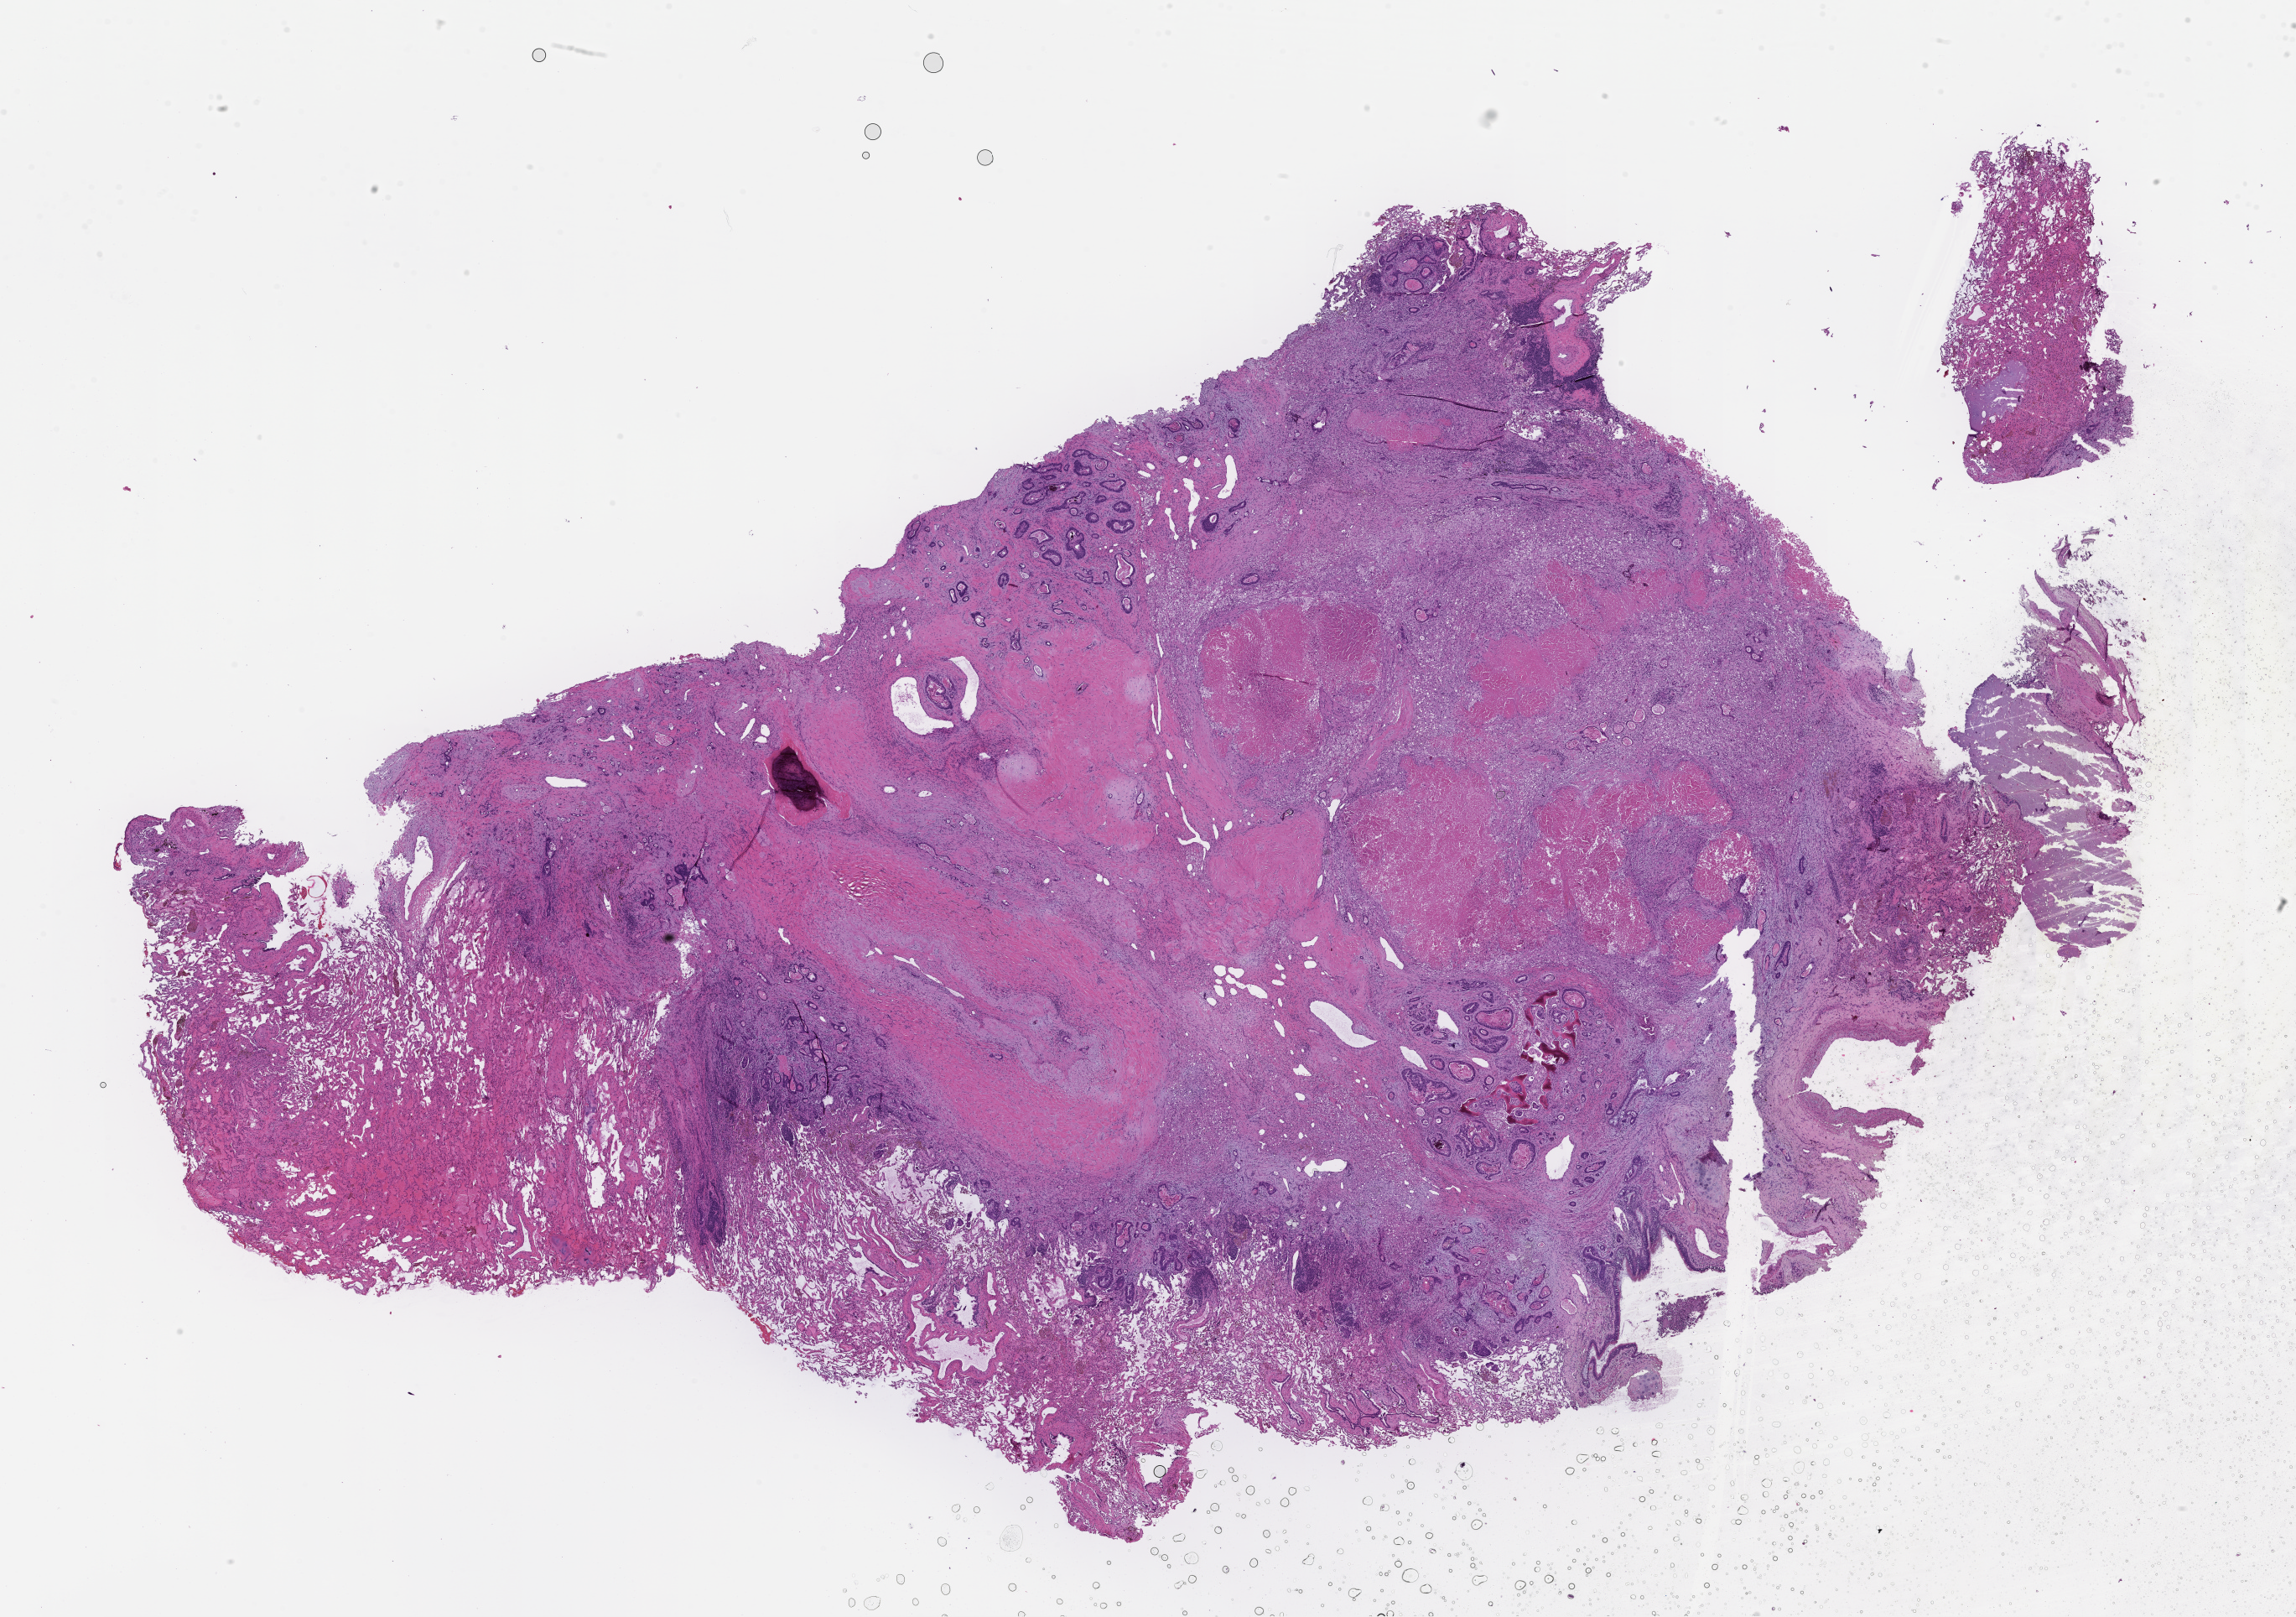
Hematoxylin and eosin (H&E) whole-slide image — a low-resolution overview of the entire scanned area, about 22.1 x 15.6 mm. Formalin-fixed paraffin-embedded section. Specimen time point: collected on treatment. Patient: male.
This section: metastasis (sampled organ not recorded). Patient diagnosis (primary): Colorectal Carcinoma.